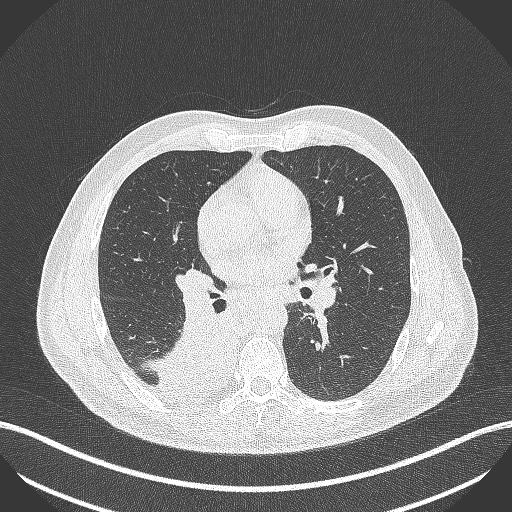
Chest CT, one axial slice. Position 253 of 451 along the scan axis. Reconstruction kernel B70f. Lung window (W 1500 / L -600 HU). 1 mm slice thickness. 512 × 512 image matrix. Male patient, age 61 years. From the clinical record (not read from this slice): clinical TNM (as recorded): T1 N0 M0; histopathological grade: G3.
Outlined on this slice (rectangle marked by the reading radiologist):
- lung tumour (recorded histology: small cell carcinoma): box from (x=142, y=304) to (x=242, y=410) px